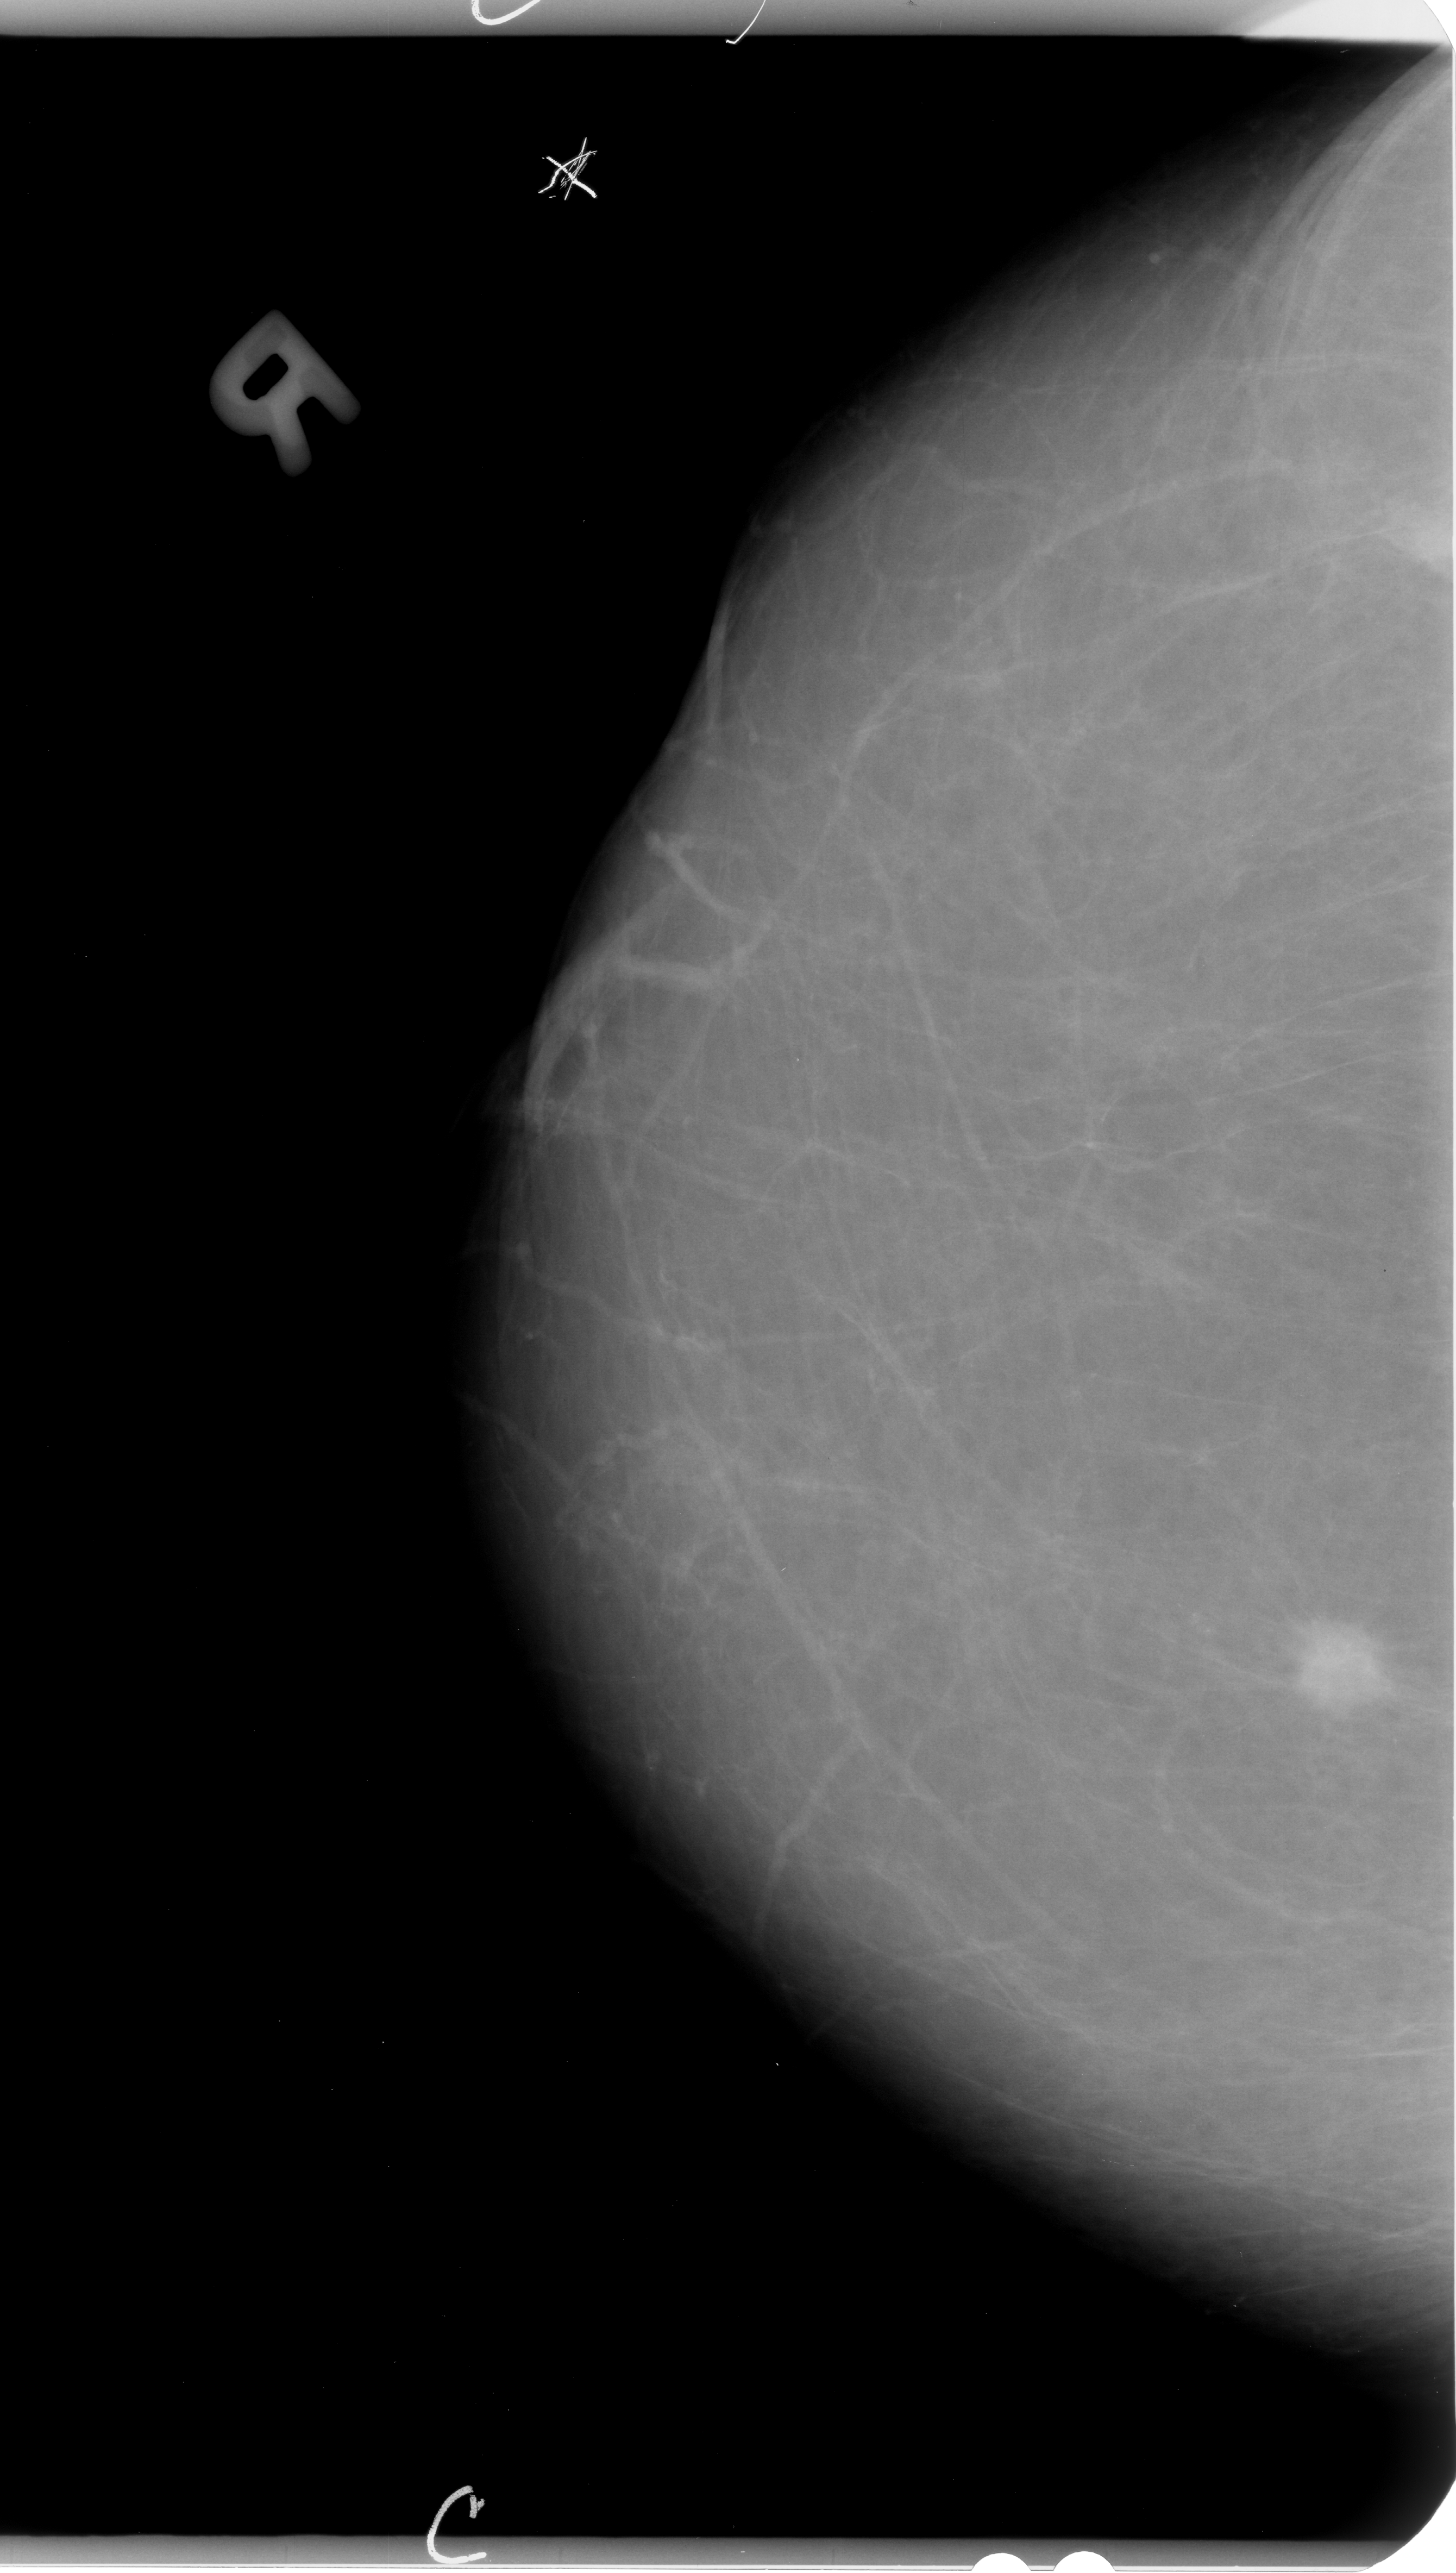
Mammogram (digitized film). Right breast. Craniocaudal (CC) view. BI-RADS breast density category 1 (scale 1–4). 1456 × 2573 image matrix.
Expert-marked regions of interest on this image (one box per marked abnormality):
- mass, shape irregular, margins spiculated; BI-RADS assessment category 4; subtlety rating 5 on a 1 (subtle) to 5 (obvious) scale; pathology (as recorded): malignant: bounding box <1263,1606,1411,1738> (left, top, right, bottom; pixels)